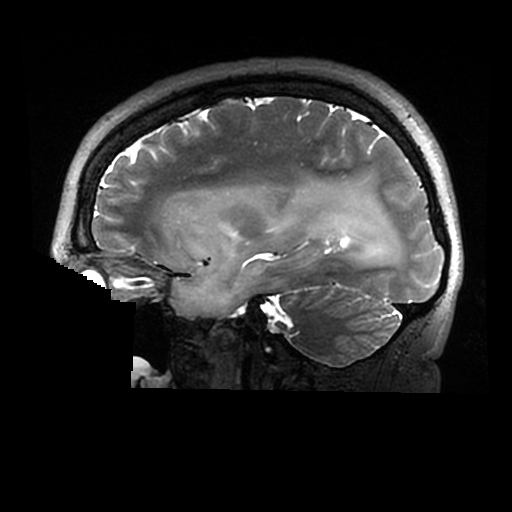
Brain MRI from a brain-tumour surgery series, one sagittal slice. 0.6 mm slice thickness. 512 × 512 image matrix, field of view 240 × 240 mm. Case-level facts recorded for this patient, not image findings: histopathology: Astrocytoma; WHO grade: 2; IDH mutation: yes.
Annotated regions visible in this slice (outlined manually by an expert reader):
- tumour: box from (x=171, y=183) to (x=401, y=319) px